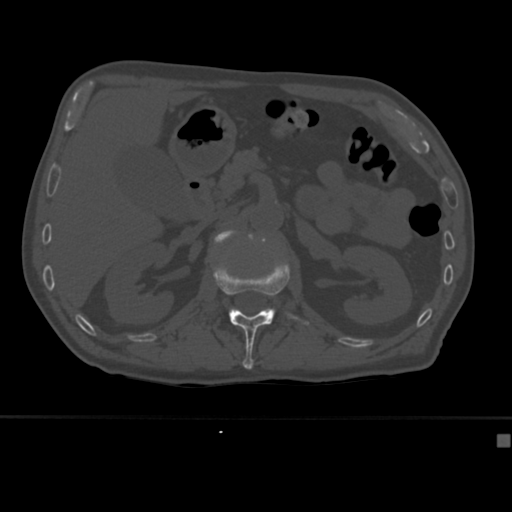
CT including the spine, one axial slice. Position 166 of 430 along the scan axis. Bone window (W 1800 / L 400 HU). 512 × 512 image matrix, field of view 337 × 337 mm. Male patient, age 64 years. Case-level facts recorded for this patient, not image findings: primary cancer: uterus; vertebrae with lytic lesions (as recorded): T1, T4, T5, T7, L5.
Structures marked on this image (semi-automatically segmented with operator editing):
- L1 vertebra: bounding box [x1, y1, x2, y2] px = [213, 260, 309, 370]
- L2 vertebra: [214, 230, 256, 245]